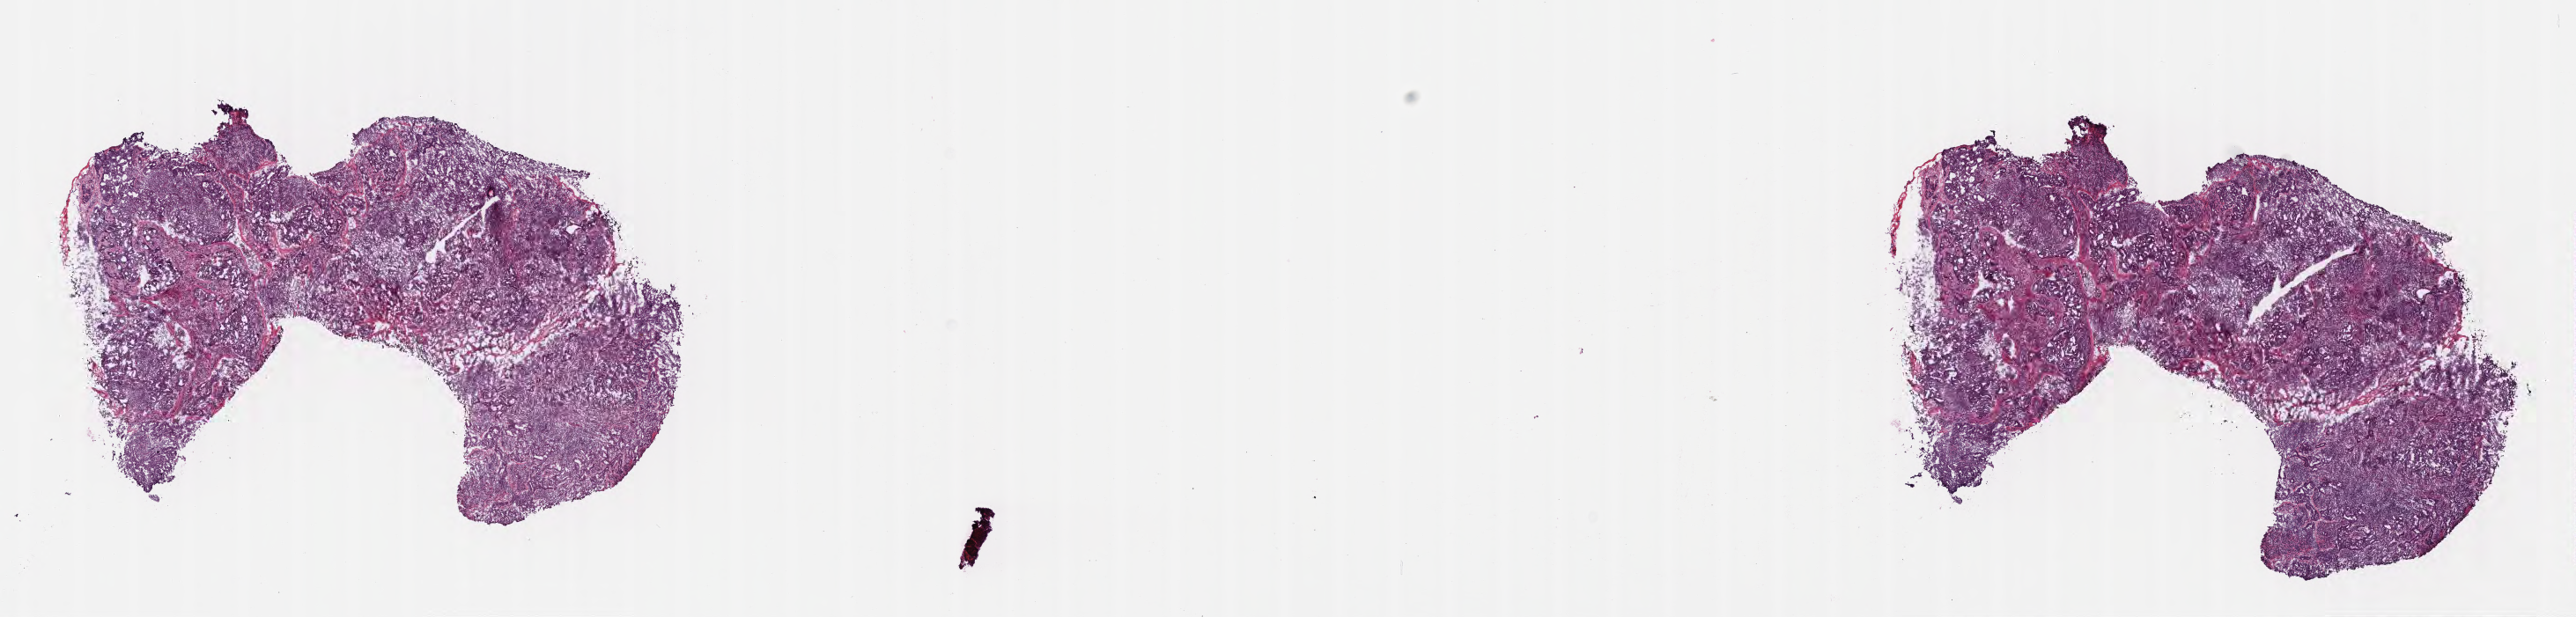
Digitized H&E-stained section — whole scanned area (about 23.6 x 5.7 mm) shown as a low-resolution overview; frozen section; metastatic tumor tissue, resected from lymph nodes of axilla or arm. Patient: female, age at initial diagnosis 83 years. Pathologist review of this section (percent, as recorded): tumor cells 85%, tumor nuclei 85%, stromal cells 15%, necrosis 0%, normal cells 0%. Inflammatory infiltration, as recorded: lymphocyte infiltration 10%, monocyte infiltration 1%, neutrophil infiltration 1%.
• patient diagnosis (primary): Infiltrating duct carcinoma, NOS